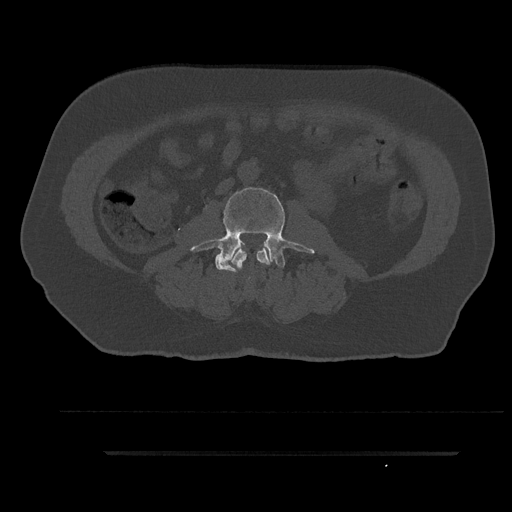
CT including the spine, one axial slice. Reconstruction kernel Br40s/3. 120 kVp. Bone window (W 1800 / L 400 HU). 0.5 mm slice thickness. 512 × 512 image matrix, field of view 432 × 432 mm. Patient: male, 63 years. Case-level facts recorded for this patient, not image findings: primary cancer: renal.
Annotated regions visible in this slice (semi-automatic segmentation, software-assisted and operator-edited):
- L2 vertebra: bounding box <231,248,270,272> (left, top, right, bottom; pixels)
- L3 vertebra: <190,185,314,272>